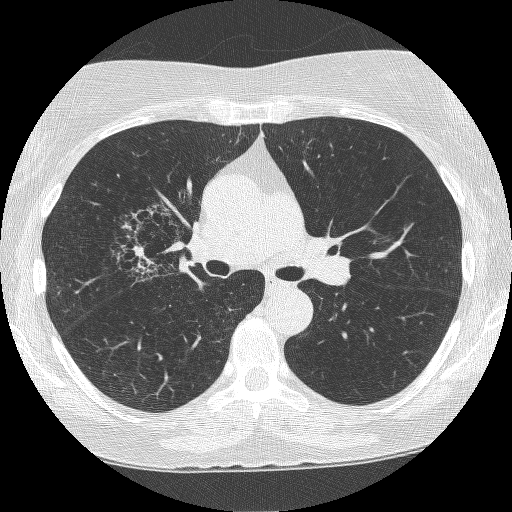
Chest CT (low-dose screening protocol), one axial image. Second annual screen. Lung window (W 1500 / L -600 HU). Lung (sharp) reconstruction kernel (BONE). Slice 148 of 249 in the series. 512 × 512 image matrix. Female participant, aged 64 years at enrolment. Former smoker at enrolment.
Lesion marked by an expert reader, bounding box <116,205,204,289> (left, top, right, bottom; pixels). The screening reader recorded 4 non-calcified nodules or masses ≥4 mm on this exam (right upper lobe, right upper lobe, right upper lobe, left upper lobe); which of them this box marks is not recorded. Later outcome: lung cancer diagnosed 381 days after this screen — adenocarcinoma, NOS, right upper lobe, right middle lobe, right hilum, stage IV (AJCC 6th edition), 85 mm at pathology.